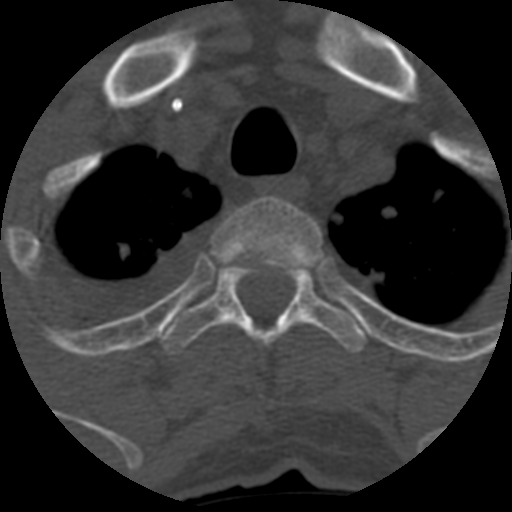
CT including the spine, one axial slice; slice 494 of 708 in the series (ordered by position); 120 kVp; one of 3 acquisitions stored at this slice position; bone window (W 1800 / L 400 HU); 512 × 512 image matrix. Patient age 55 years. From the clinical record (not read from this slice): primary cancer: colon.
Annotated regions visible in this slice (semi-automatic segmentation, software-assisted and operator-edited):
- T2 vertebra: bounding box [x1, y1, x2, y2] px = [213, 198, 323, 269]
- T3 vertebra: [161, 263, 366, 353]